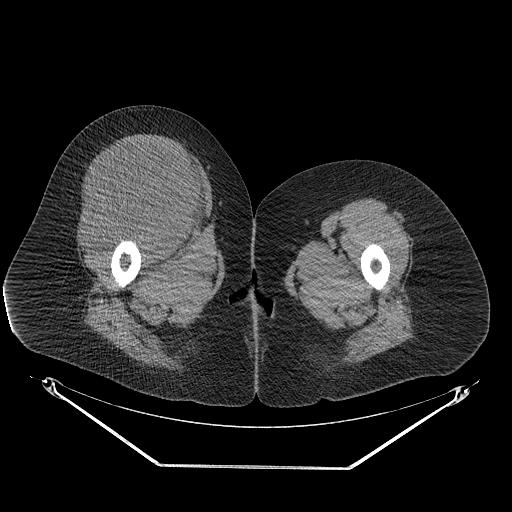
CT of an extremity soft-tissue mass (from a PET/CT study), one axial slice. Reconstruction kernel STANDARD. Soft-tissue window (W 400 / L 40 HU). 3.75 mm slice thickness. 512 × 512 image matrix. Female patient. From the clinical record (not read from this slice): histological type: malignant solitary fibrous tumor; grade: intermediate; site of the primary tumour: right thigh.
Annotated regions visible in this slice (expert contour drawn on MRI and transferred to this co-registered scan by the dataset authors):
- gross tumour volume including surrounding oedema: bounding box <78,142,207,239> (left, top, right, bottom; pixels)
- gross tumour volume (mass): <84,142,204,238>